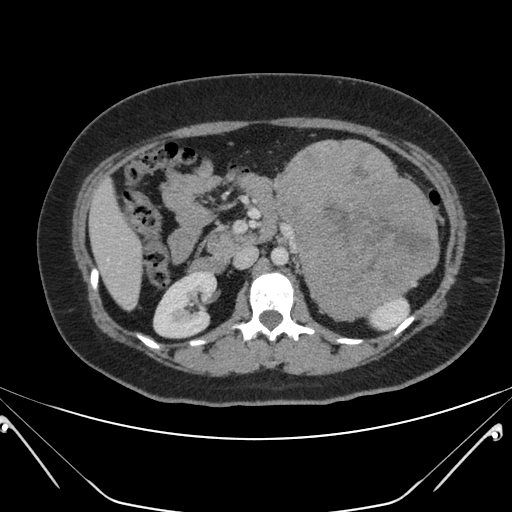
Contrast-enhanced abdominal CT, one axial slice; 120 kVp; intravenous contrast given; soft-tissue window (W 400 / L 40 HU); 3 mm slice thickness; 512 × 512 image matrix, field of view 394 × 394 mm. Patient: female, 26 years. From the clinical record (not read from this slice): diagnosis: adrenocortical carcinoma; tumour side: left adrenal; tumour size at pathology: 28 cm; Ki-67 index: 20 %; stage (as recorded): 2.
Outlined on this slice (semi-automatically segmented with operator editing):
- mass: bounding box <274,139,439,321> (left, top, right, bottom; pixels)